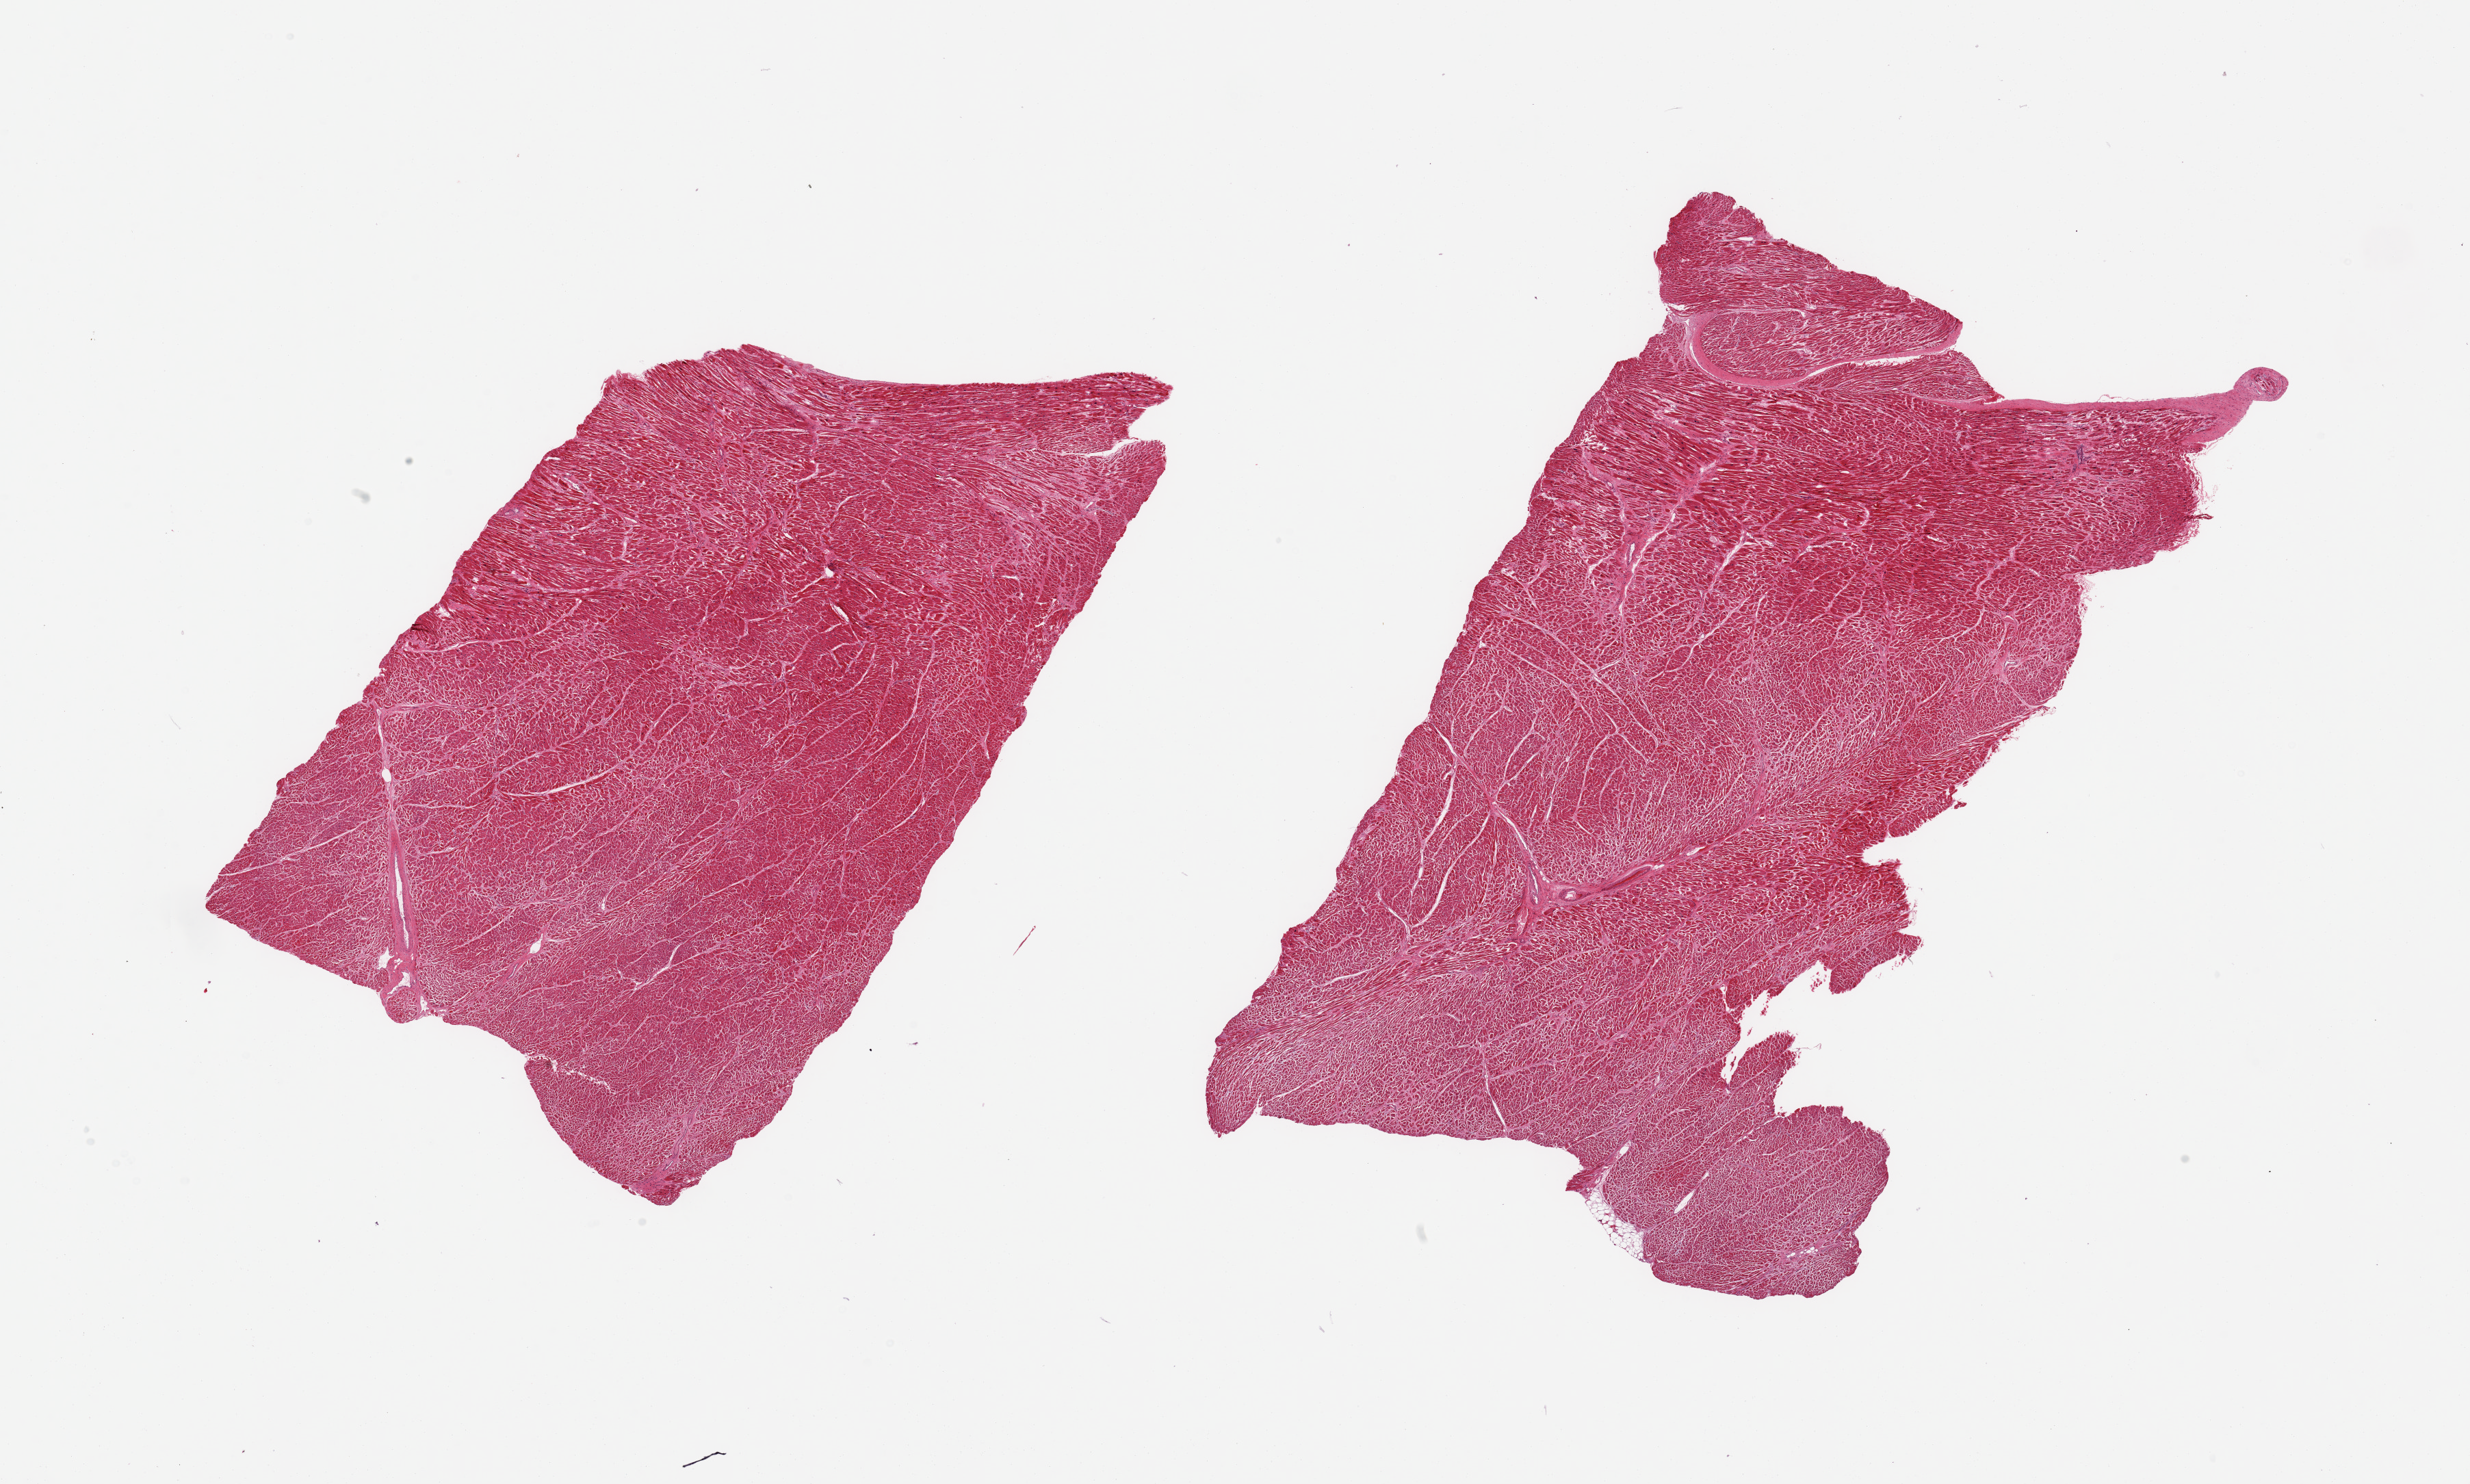
H&E whole-slide image, brightfield, whole scanned area (about 28.5 x 17.2 mm, acquisition: 20x scan) shown as a low-resolution overview, PAXgene-fixed paraffin-embedded (PFPE) section, target tissue: heart, donor tissue sample. Male donor.
• reviewer comment on this tissue sample: 2 pieces; scattered patchy areas of mild interstitial fibrosis [<5%]; hypereosinophilic fibers suggestive of early ischemia